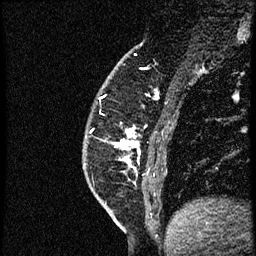
Breast MRI (dynamic contrast-enhanced), one sagittal slice. Dynamic contrast-enhanced study with each time point stored as its own series, time point 2 of 4 at this slice position (early post-contrast, ordered by acquisition time). 1.5 T. TE 4.2 ms, TR 18.9 ms. 2 mm slice thickness. 256 × 256 image matrix, field of view 200 × 200 mm. Female patient. Case-level facts recorded for this patient, not image findings: setting: breast cancer imaged before/during neoadjuvant chemotherapy; receptor status: HER2-positive.
Annotated regions visible in this slice (semi-automatically segmented with operator editing):
- analysis volume of interest (the breast-tissue region the enhancement analysis was run in; not a lesion): bounding box [x1, y1, x2, y2] px = [118, 91, 172, 189]
- tumour enhancement mask (voxels above the 100 % enhancement threshold inside the analysis volume of interest): [118, 129, 141, 162]